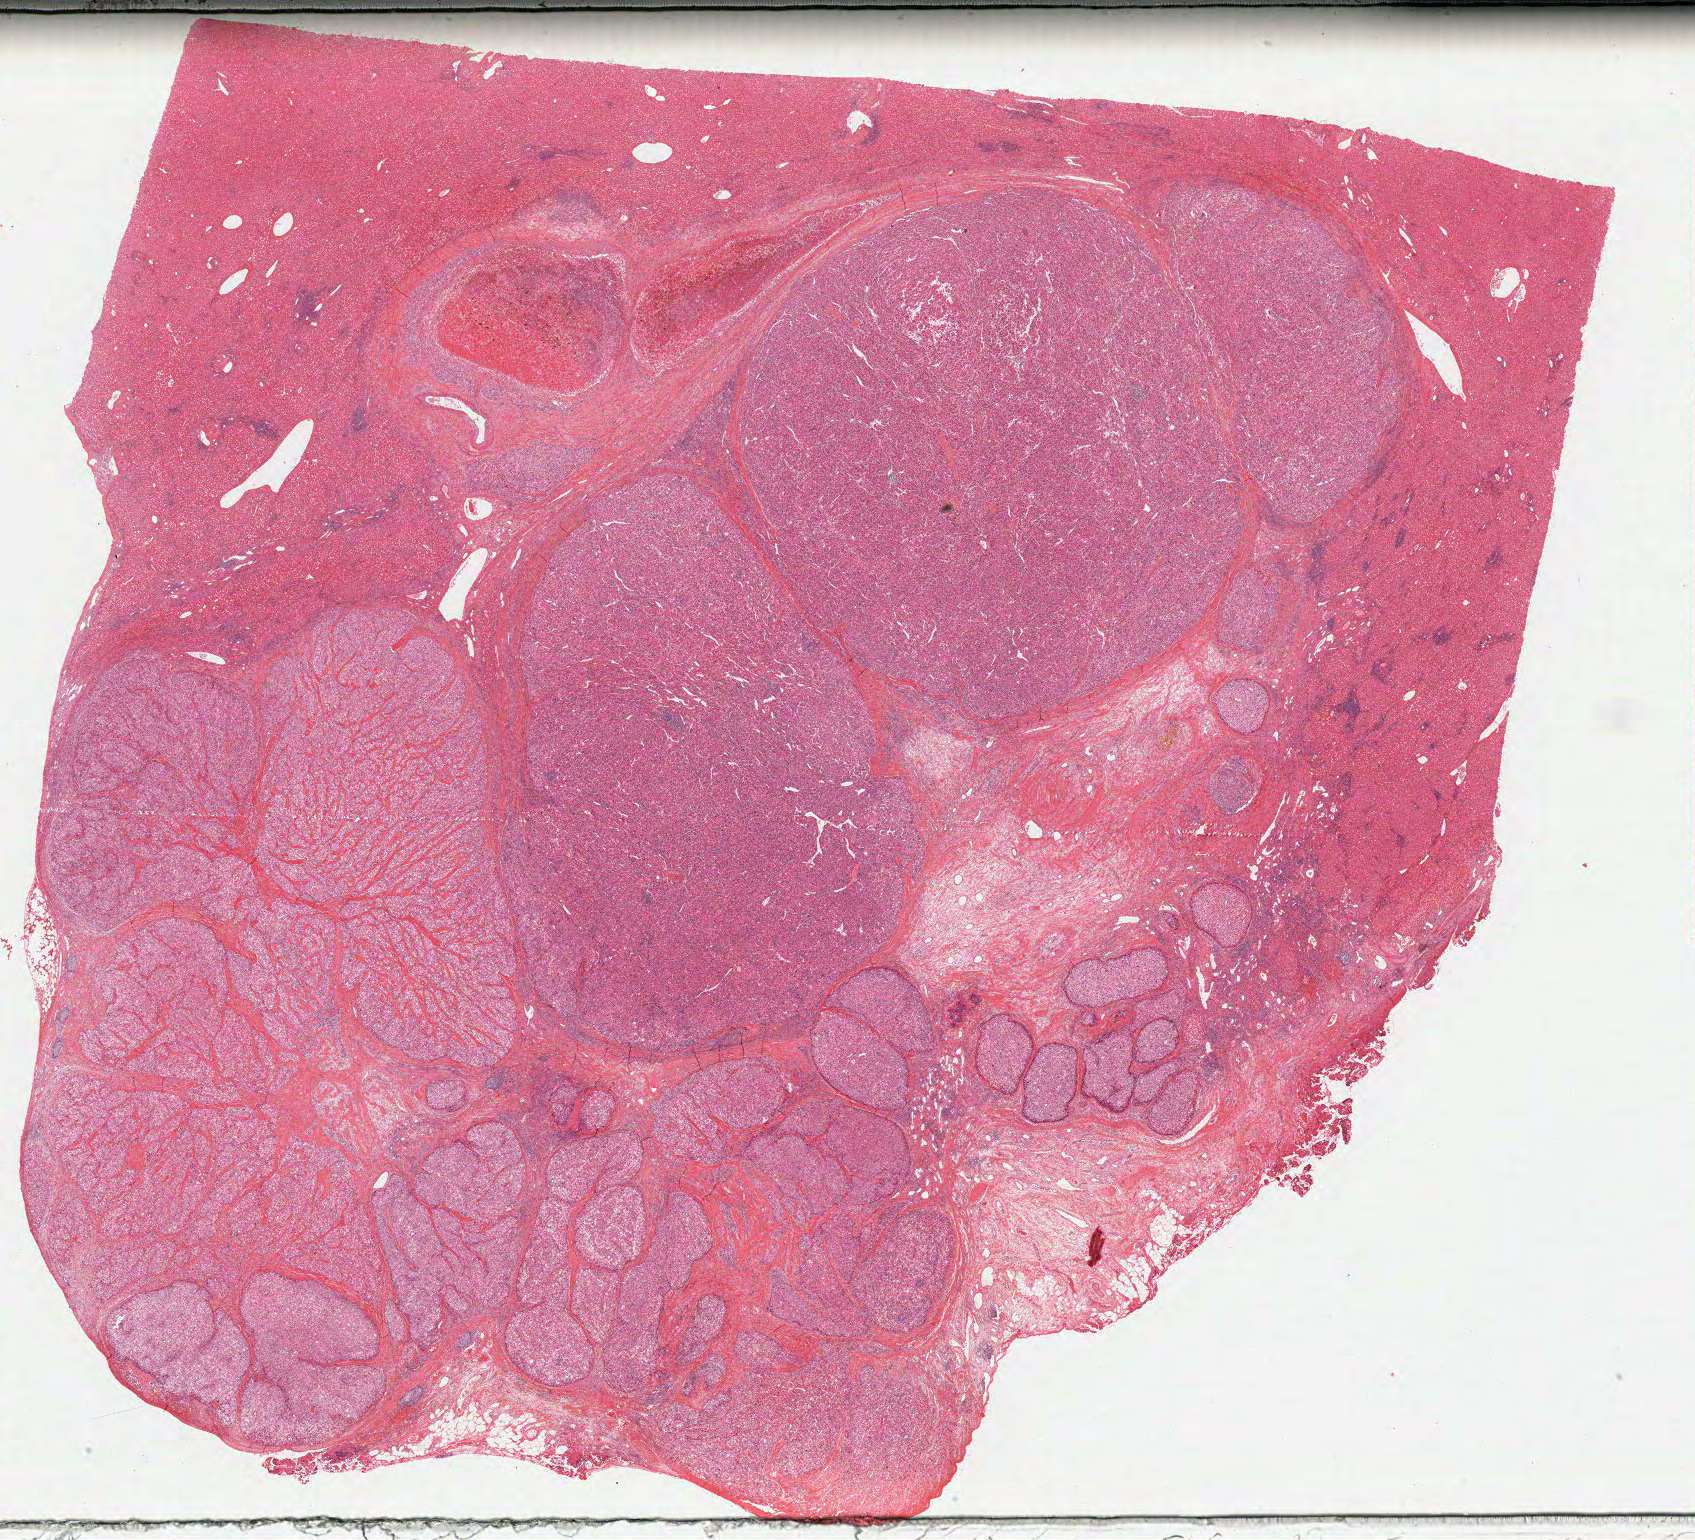
H&E whole-slide image — low-resolution overview of the scanned area, about 26.8 x 24.4 mm; formalin-fixed paraffin-embedded (FFPE) diagnostic section; liver, primary tumour sample. Male patient; age at initial diagnosis 56 years. Histologic grade: G3 (poorly differentiated).
* AJCC pathologic stage: II (6th edition)
* diagnosis: Hepatocellular carcinoma, NOS